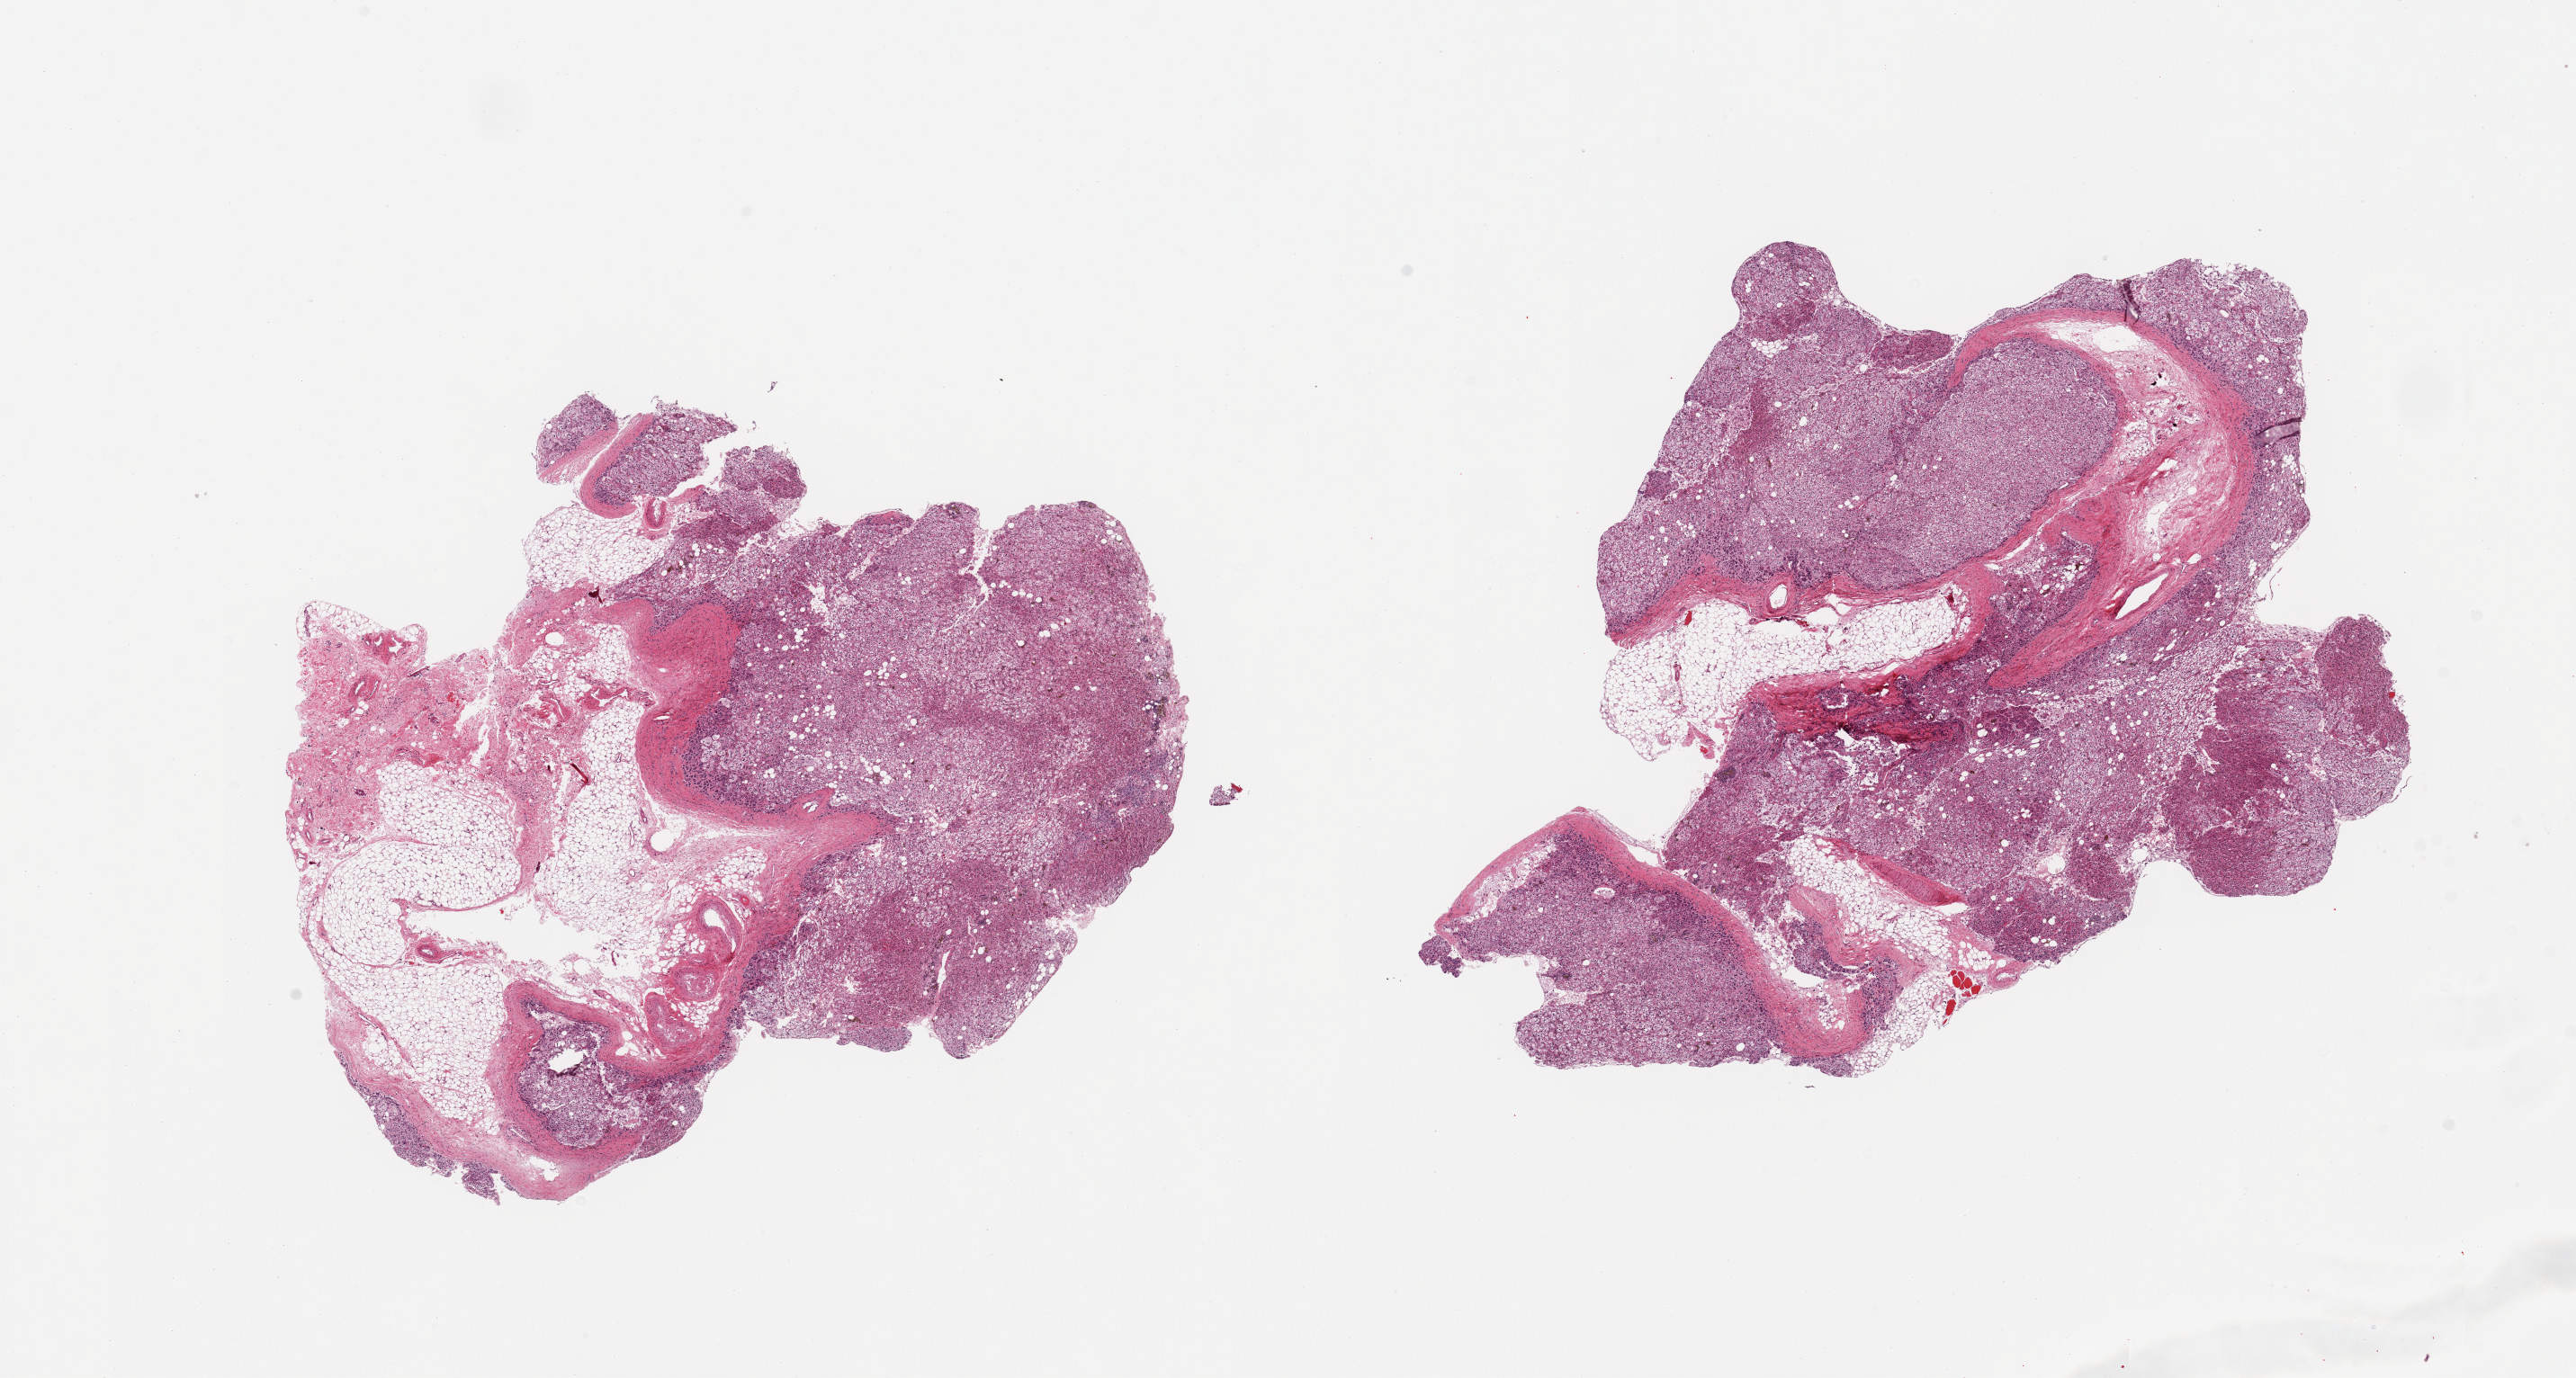
Digitized hematoxylin and eosin (H&E)-stained section, low-resolution overview of the scanned area, about 22.6 x 12.1 mm. PAXgene-fixed, paraffin-embedded tissue. Section of adrenal gland (target tissue). Tissue donor sample. Donor sex: male.
Reviewer comment on this tissue sample: 2 pieces; not pancreas, adrenal gland.